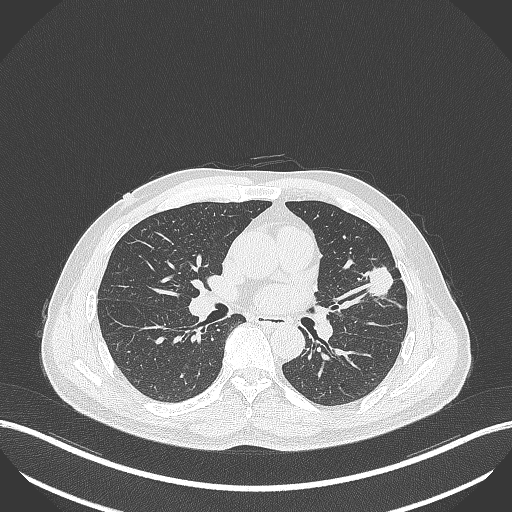
Chest CT, one axial slice; position 213 of 418 along the scan axis; 120 kVp; lung window (W 1500 / L -600 HU); 1 mm slice thickness; 512 × 512 image matrix, field of view 400 × 400 mm. Male patient, age 55 years. Case-level facts recorded for this patient, not image findings: clinical TNM (as recorded): T1c N0 M0.
Structures marked on this image (rectangle marked by the reading radiologist):
- lung tumour (recorded histology: adenocarcinoma): bounding box <363,264,398,302> (left, top, right, bottom; pixels)